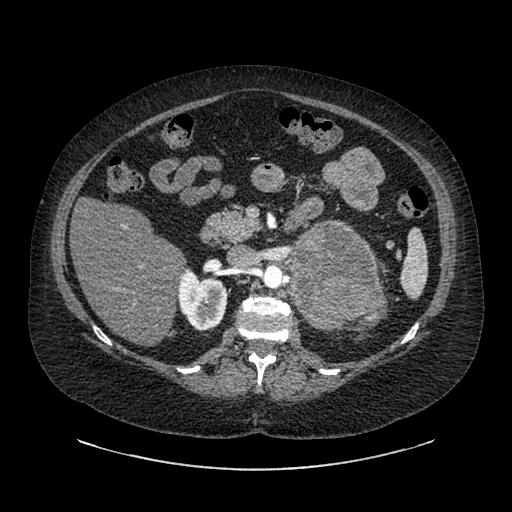
Contrast-enhanced abdominal CT, one axial slice. Slice 539 of 769 in the series (ordered by position). 120 kVp. Intravenous contrast given. Soft-tissue window (W 400 / L 40 HU). 0.62 mm slice thickness. 512 × 512 image matrix. Female patient, age 61 years. From the clinical record (not read from this slice): diagnosis: adrenocortical carcinoma; tumour side: left adrenal; tumour size at pathology: 13 cm; Ki-67 index: 79 %; stage (as recorded): 2.
Annotated regions visible in this slice (semi-automatic segmentation, software-assisted and operator-edited):
- mass: bounding box [x1, y1, x2, y2] px = [290, 224, 375, 328]